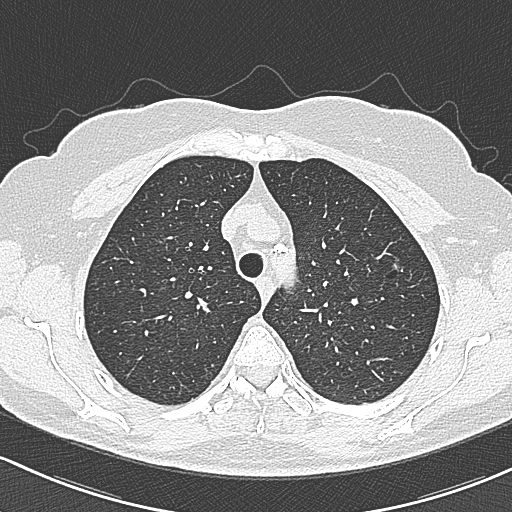
Axial slice from a low-dose chest CT screening exam, baseline screening round, lung window (W 1500 / L -600 HU), lung (sharp) reconstruction kernel (B80f), slice 72 of 312 in the series, 512 × 512 image matrix. Female participant, aged 65 years at enrolment. Current smoker at enrolment.
• Expert-annotated lung lesion, box from (x=374, y=238) to (x=415, y=285) px.
• The screening reader recorded 3 non-calcified nodules or masses ≥4 mm on this exam (left upper lobe, left upper lobe, right upper lobe); which of them this box marks is not recorded.
• Later outcome: lung cancer diagnosed 390 days after this screen — bronchiolo-alveolar carcinoma, non-mucinous, left upper lobe, stage IA (AJCC 6th edition), 10 mm at pathology.